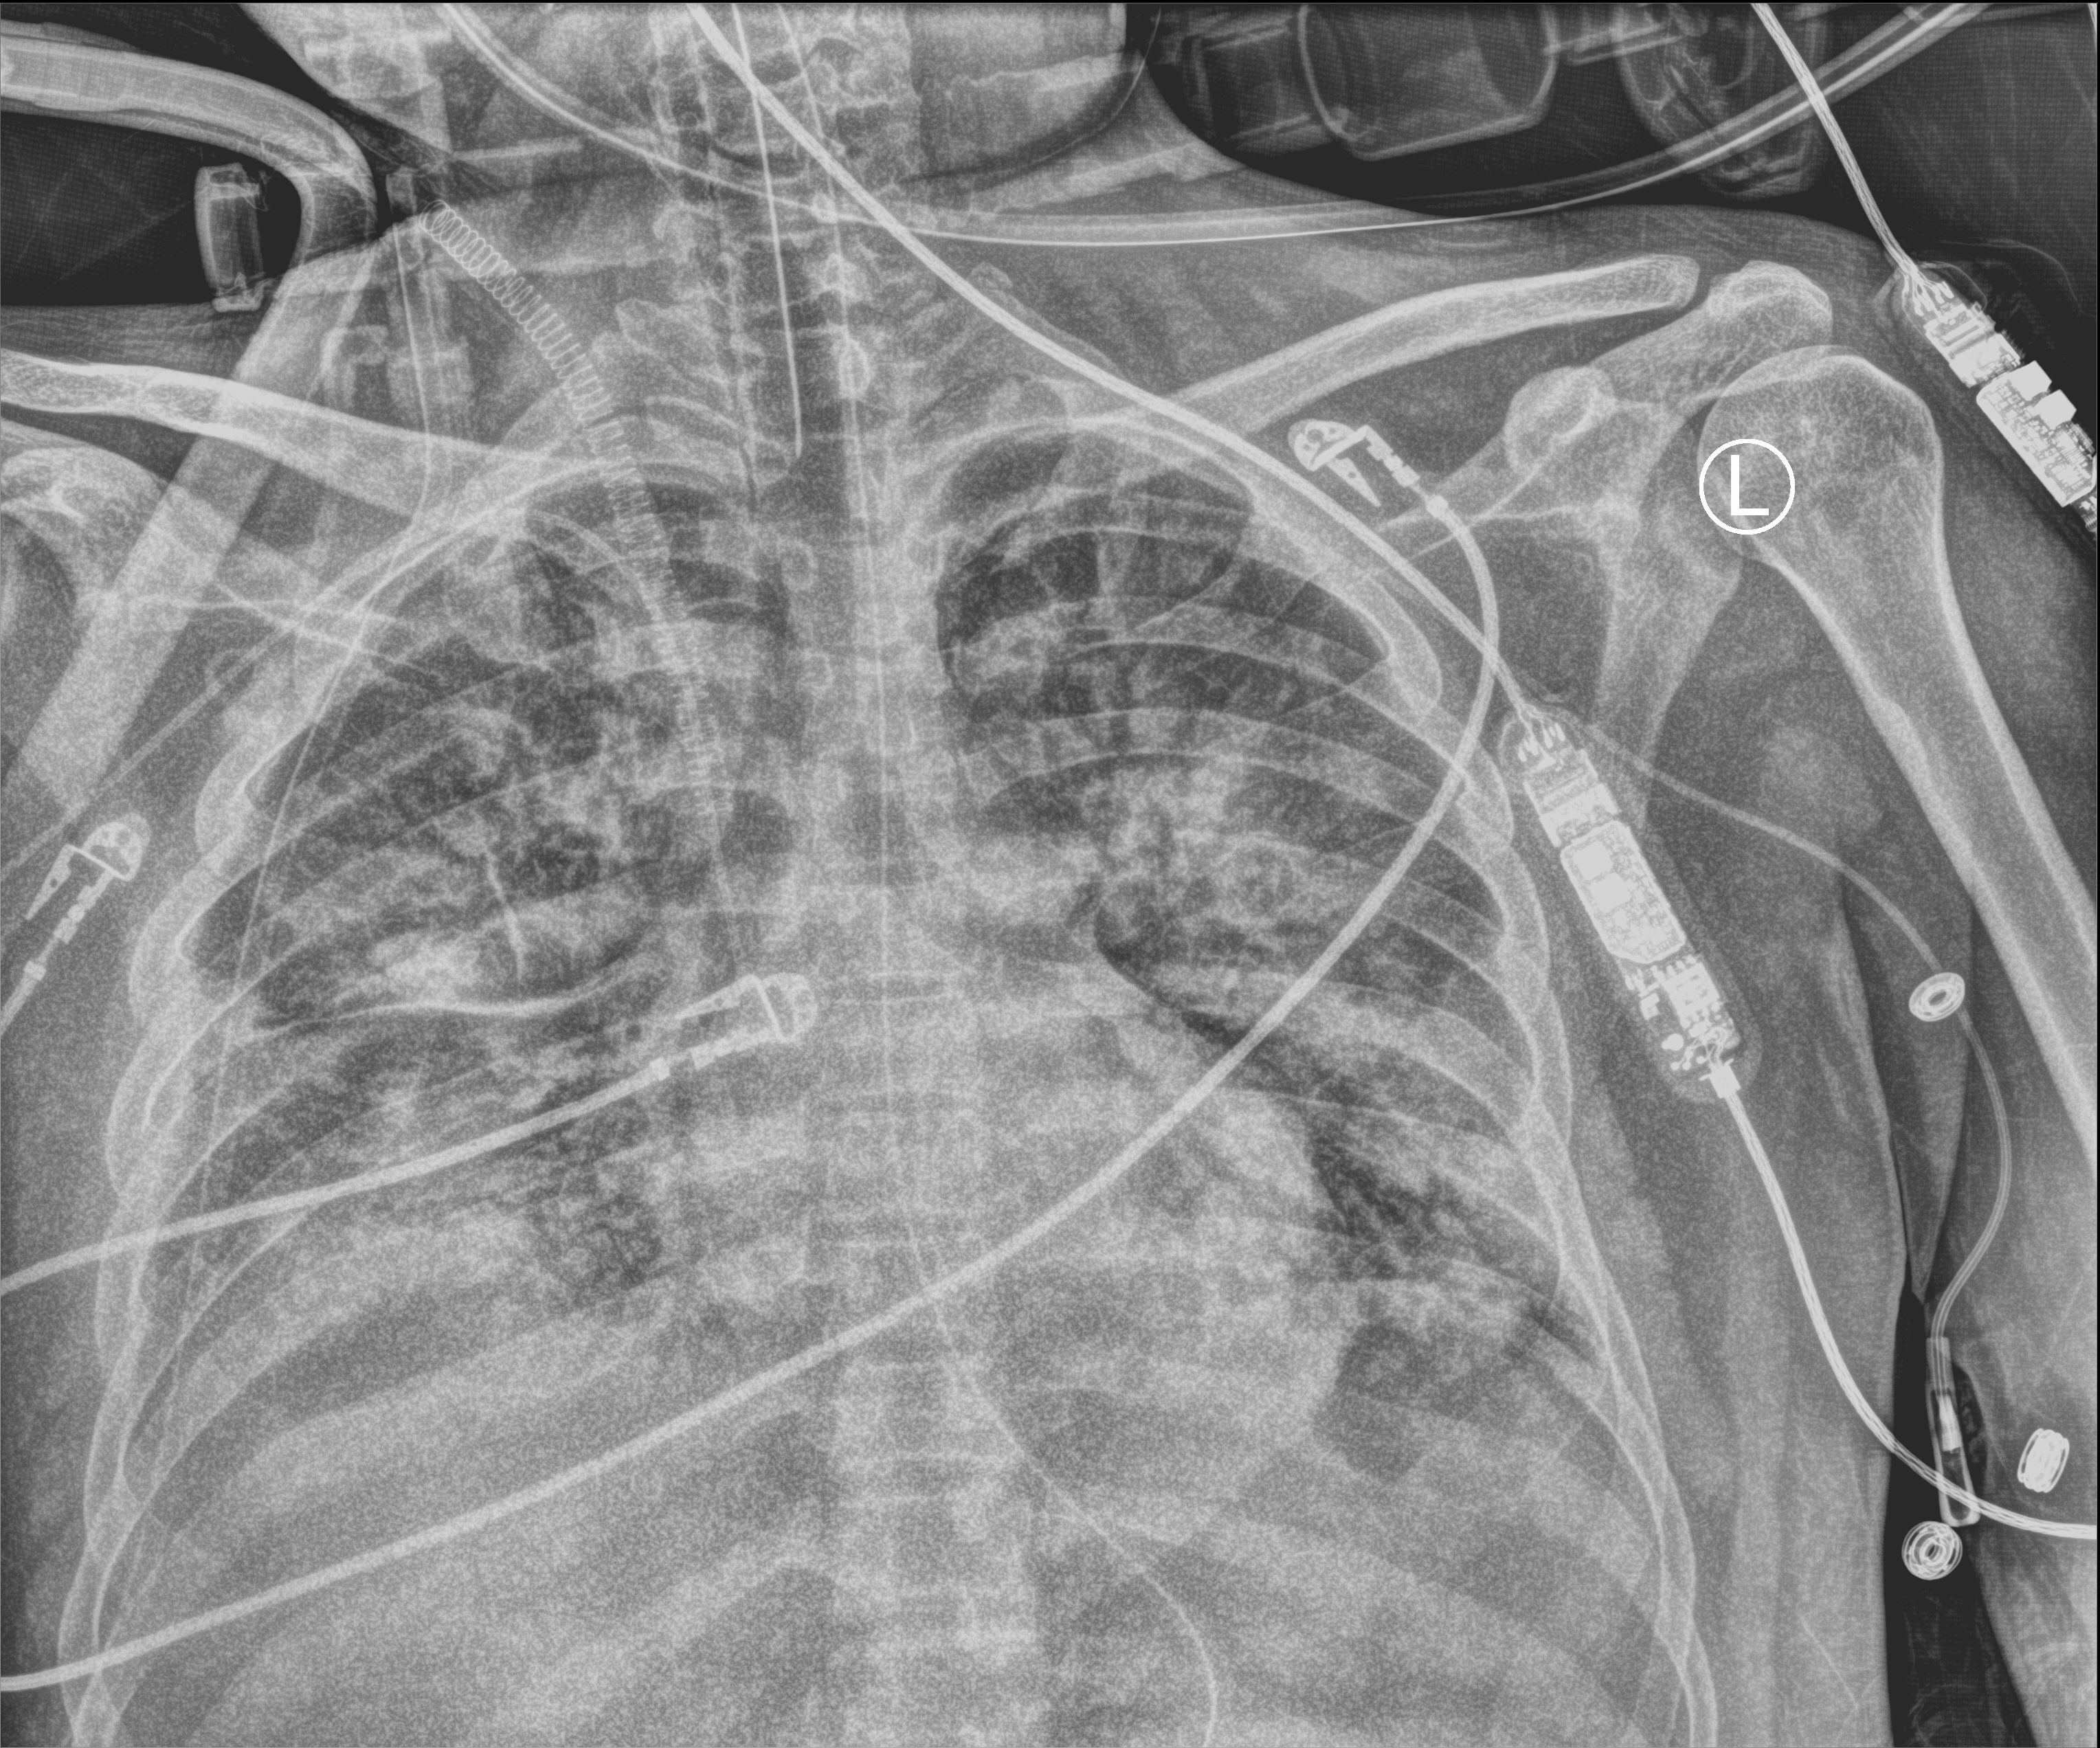
Chest X-ray (portable). Patient hospitalised with COVID-19, aged 18–59 years.
From the hospital-stay record, not from the radiograph (when in the stay this image was taken is not recorded): hypertension (admission record): no.